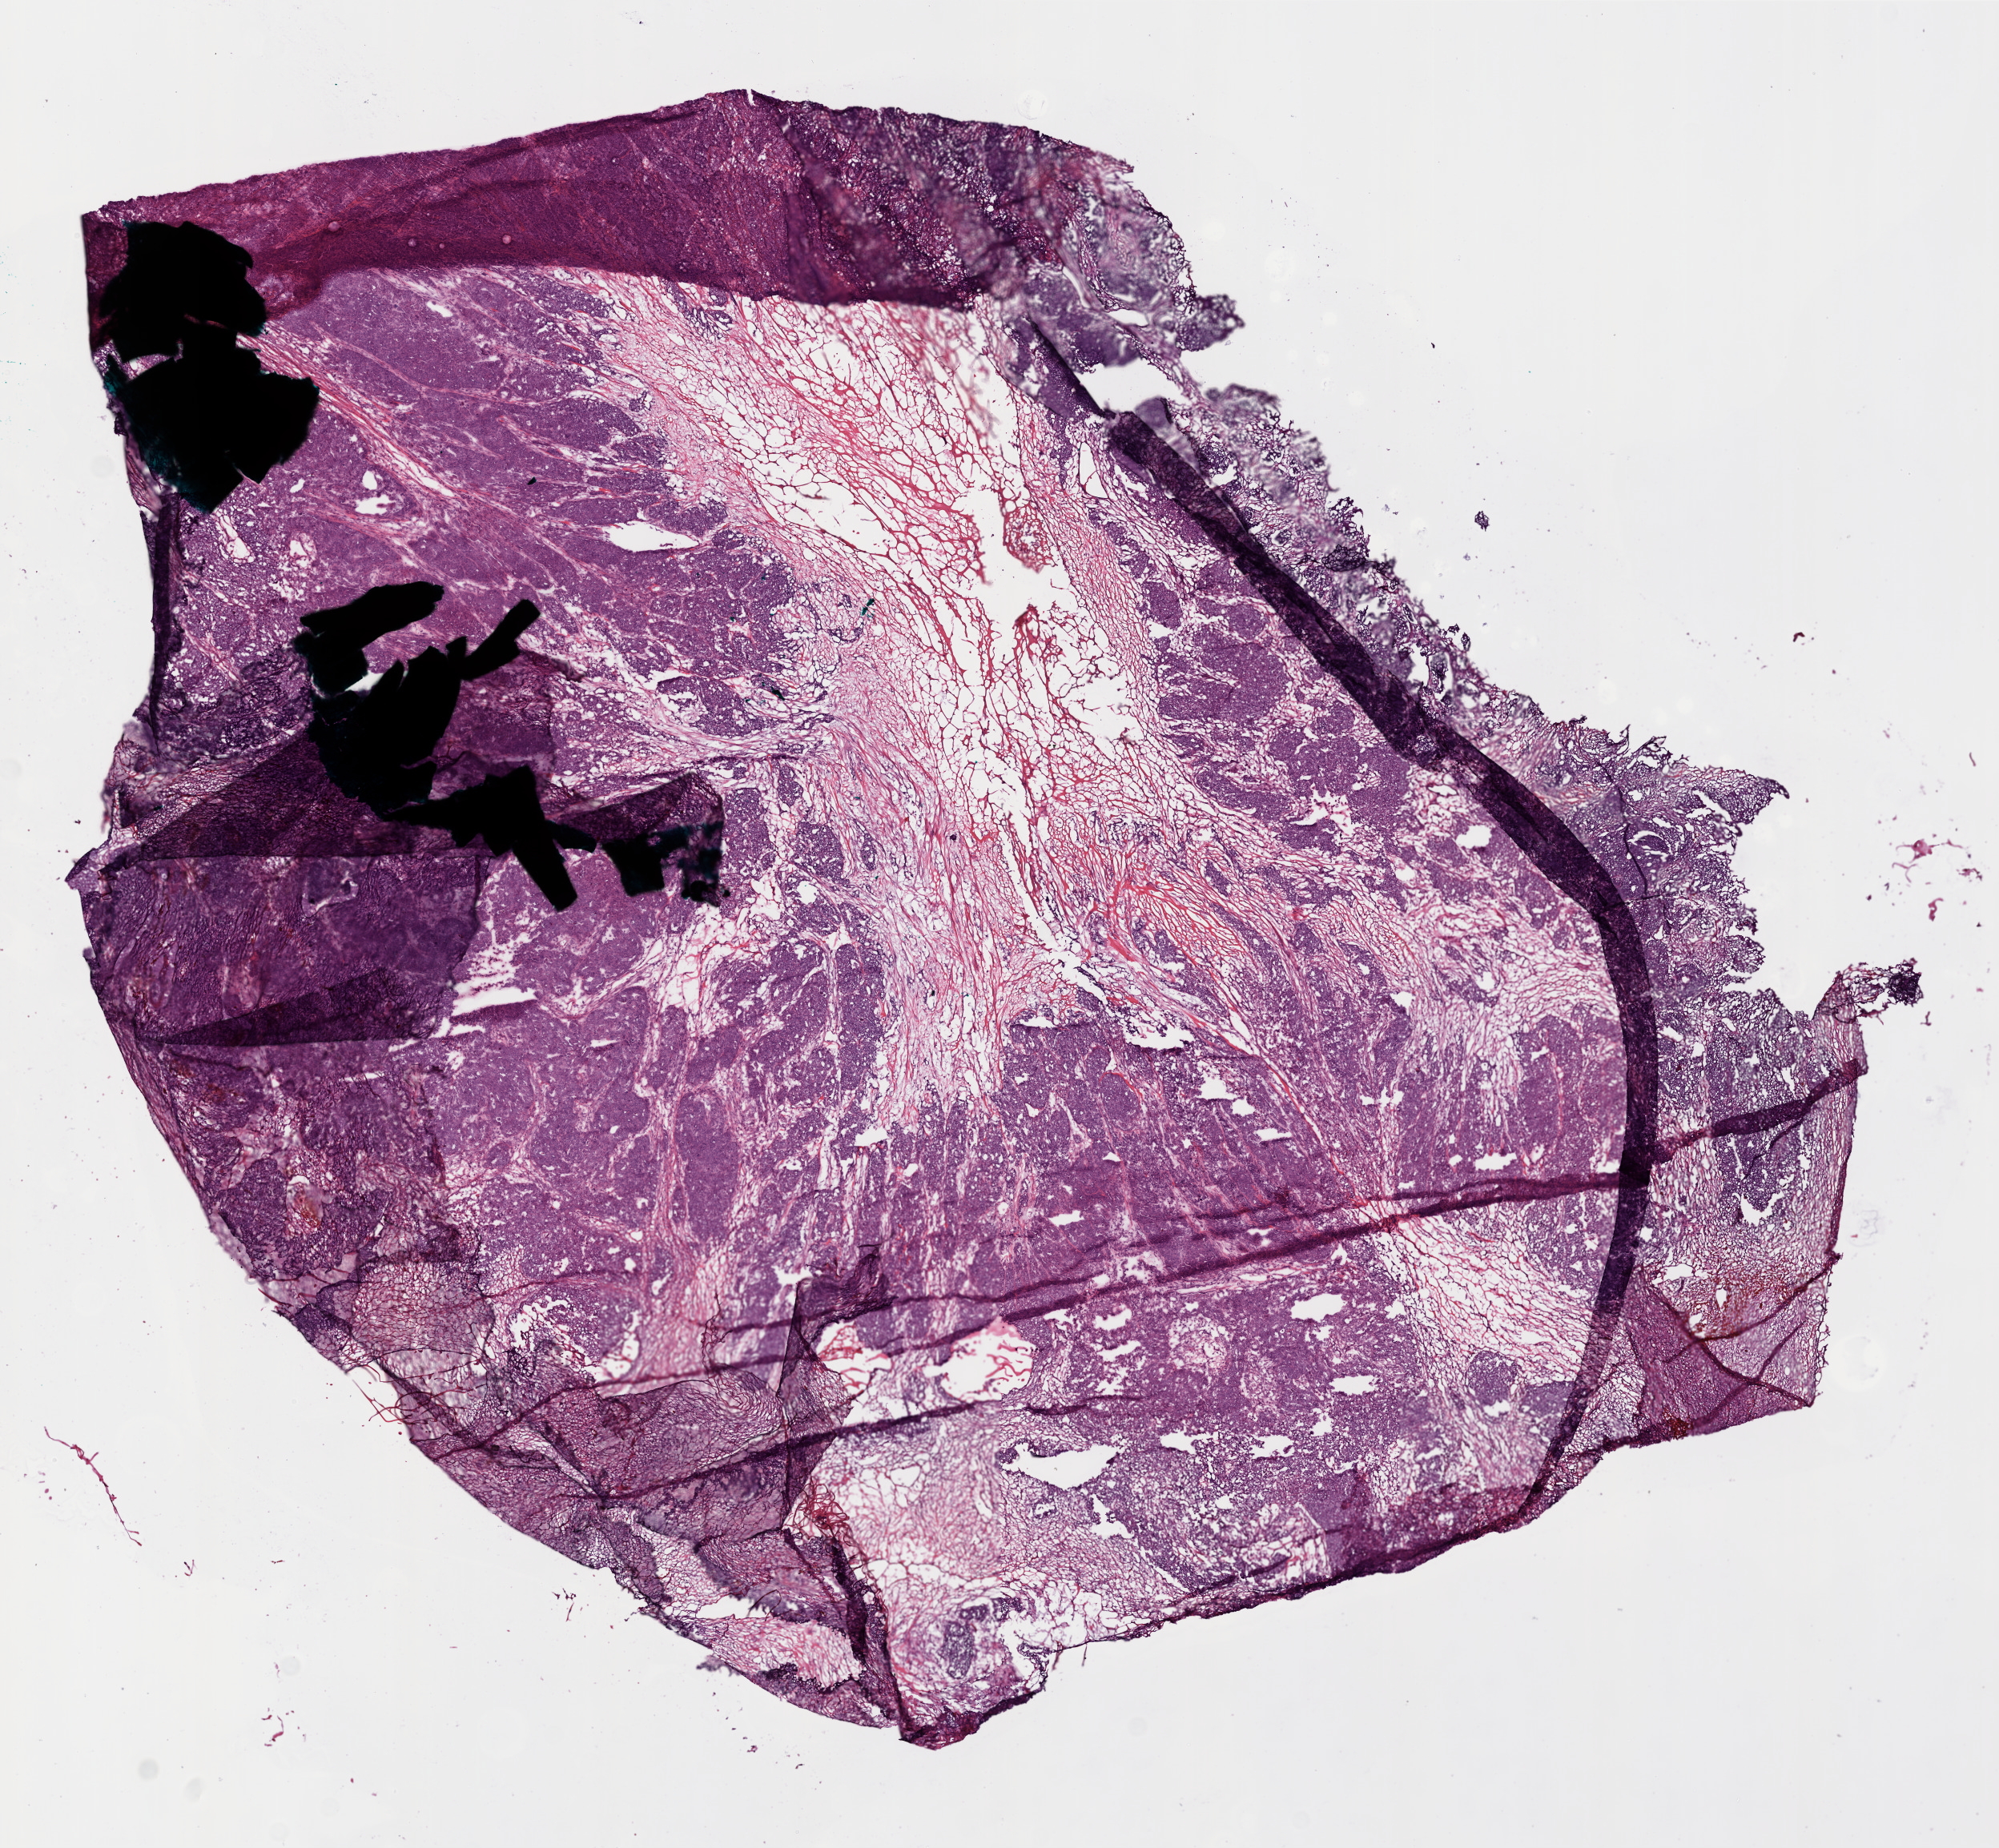
Whole-slide histology image, H&E-stained, a low-resolution overview of the entire scanned area, about 10.0 x 9.2 mm (acquisition: 20x scan), frozen section, ovary, primary tumour sample. Patient: female, age at initial diagnosis 60 years. Histologic grade: G3 (poorly differentiated). Slide review estimates, as recorded: tumour cells 0%, tumour nuclei 95%, normal cells 0%, stromal cells 0%, necrosis 10%.
• laterality: right
• FIGO stage: IIIC
• pathologic diagnosis: Serous cystadenocarcinoma, NOS